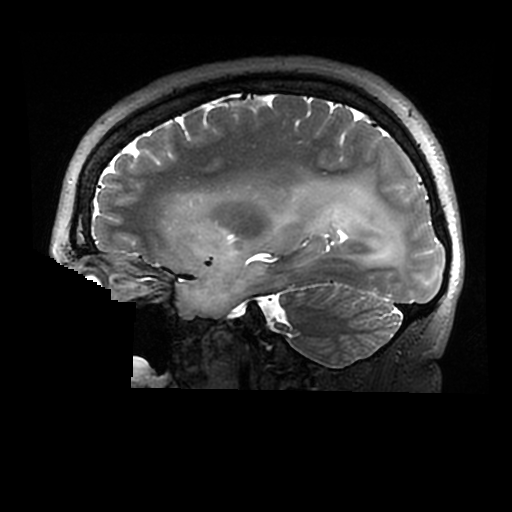
Brain MRI from a brain-tumour surgery series, one sagittal slice. Position 194 of 320 along the scan axis. 0.6 mm slice thickness. 512 × 512 image matrix, field of view 240 × 240 mm. From the clinical record (not read from this slice): histopathology: Astrocytoma; WHO grade: 2; IDH mutation: yes.
Annotated regions visible in this slice (expert manual segmentation):
- tumour: bounding box <176,183,404,317> (left, top, right, bottom; pixels)